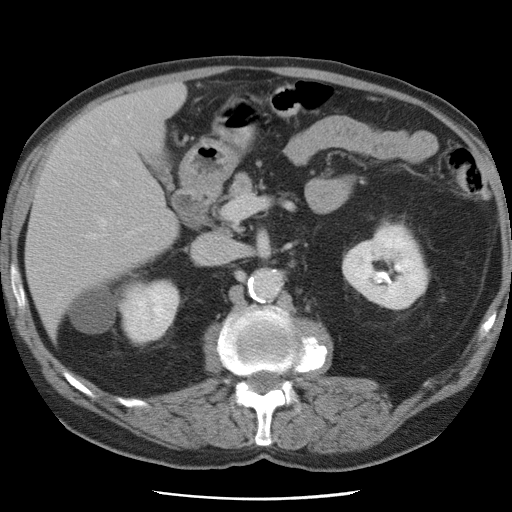
Contrast-enhanced abdominal CT, one axial slice; slice 37 of 78 in the series (ordered by position); intravenous contrast given; soft-tissue window (W 400 / L 40 HU); 5 mm slice thickness; 512 × 512 image matrix. Male patient, age 75 years. From the clinical record (not read from this slice): diagnosis: colorectal cancer liver metastases, imaged before liver resection; multiple liver metastases: yes; largest metastasis: 2.4 cm; disease in both lobes: yes.
Outlined on this slice (outlined manually by an expert reader):
- hepatic veins: bounding box <86,116,129,242> (left, top, right, bottom; pixels)
- liver: <26,84,184,332>
- planned liver remnant (the part of the liver to remain after resection): <26,117,177,334>
- portal vein (with intrahepatic branches): <112,181,116,184>